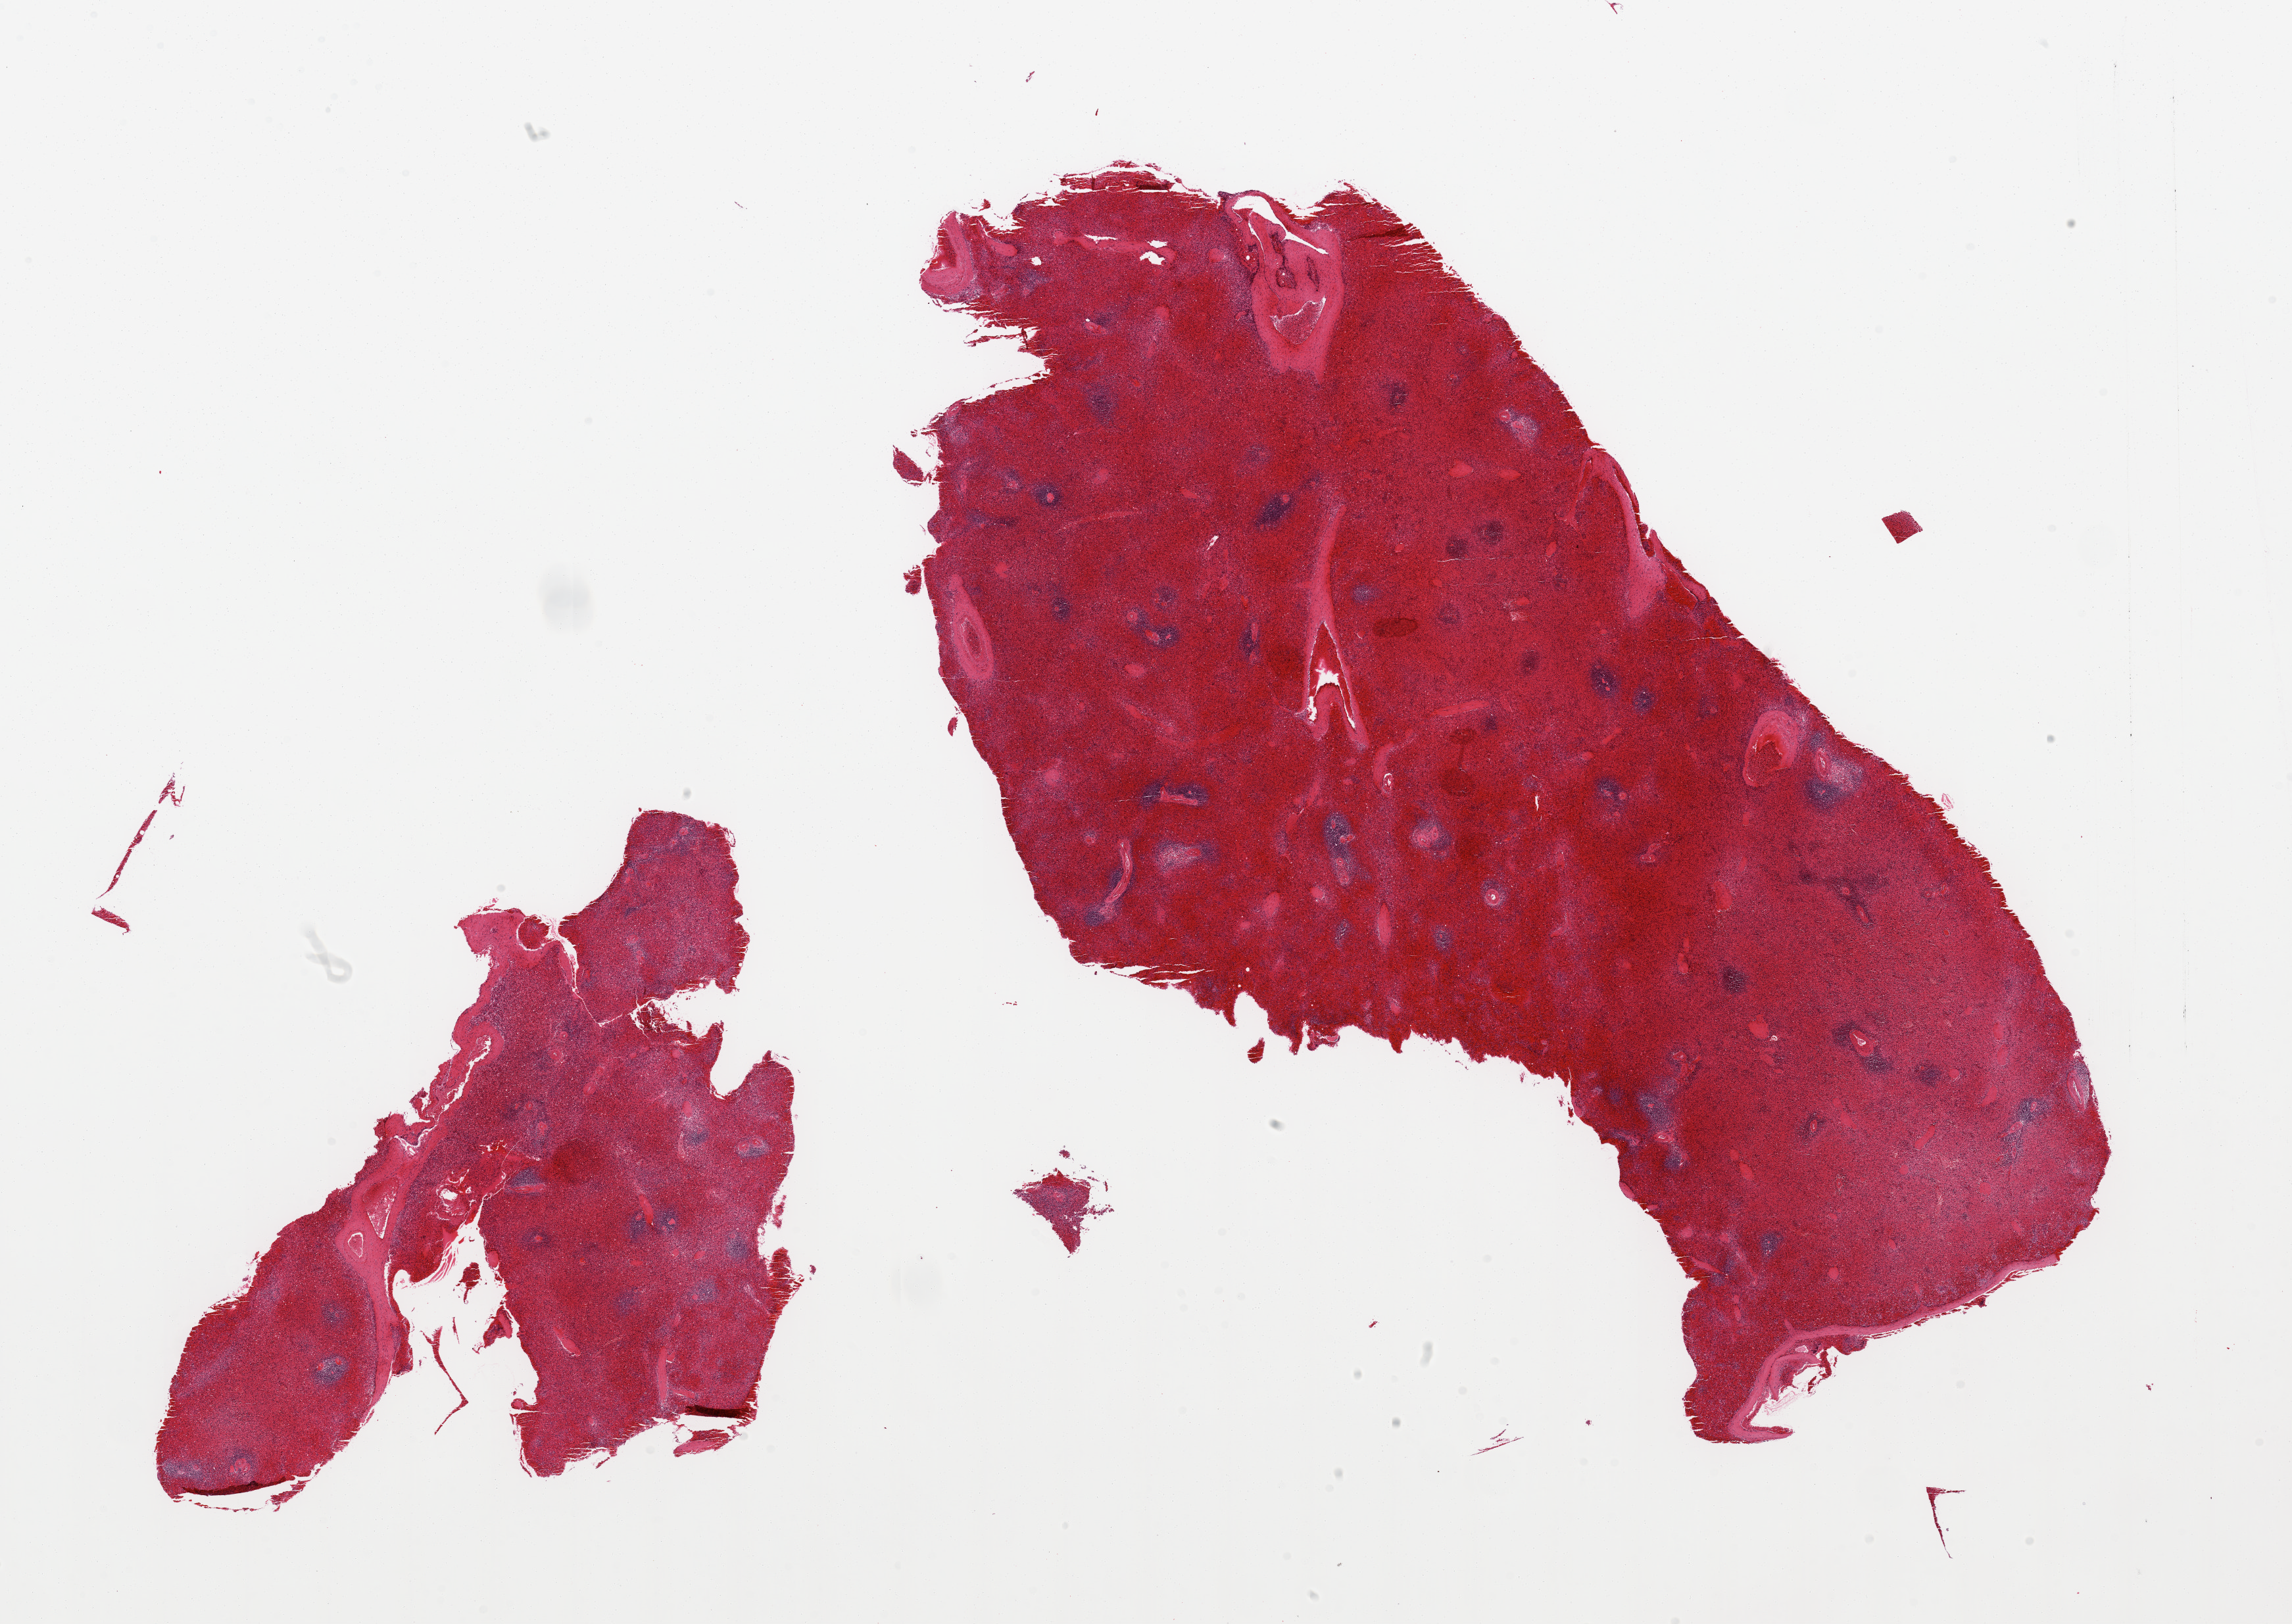
Haematoxylin and eosin whole-slide image, low-resolution overview of the scanned area, about 27.6 x 19.5 mm (from a 20x scan). PAXgene-fixed, paraffin-embedded tissue. Section of spleen (target tissue). Tissue donor sample. Donor sex: male.
Review note (as recorded): 2 pieces, marked congestion.